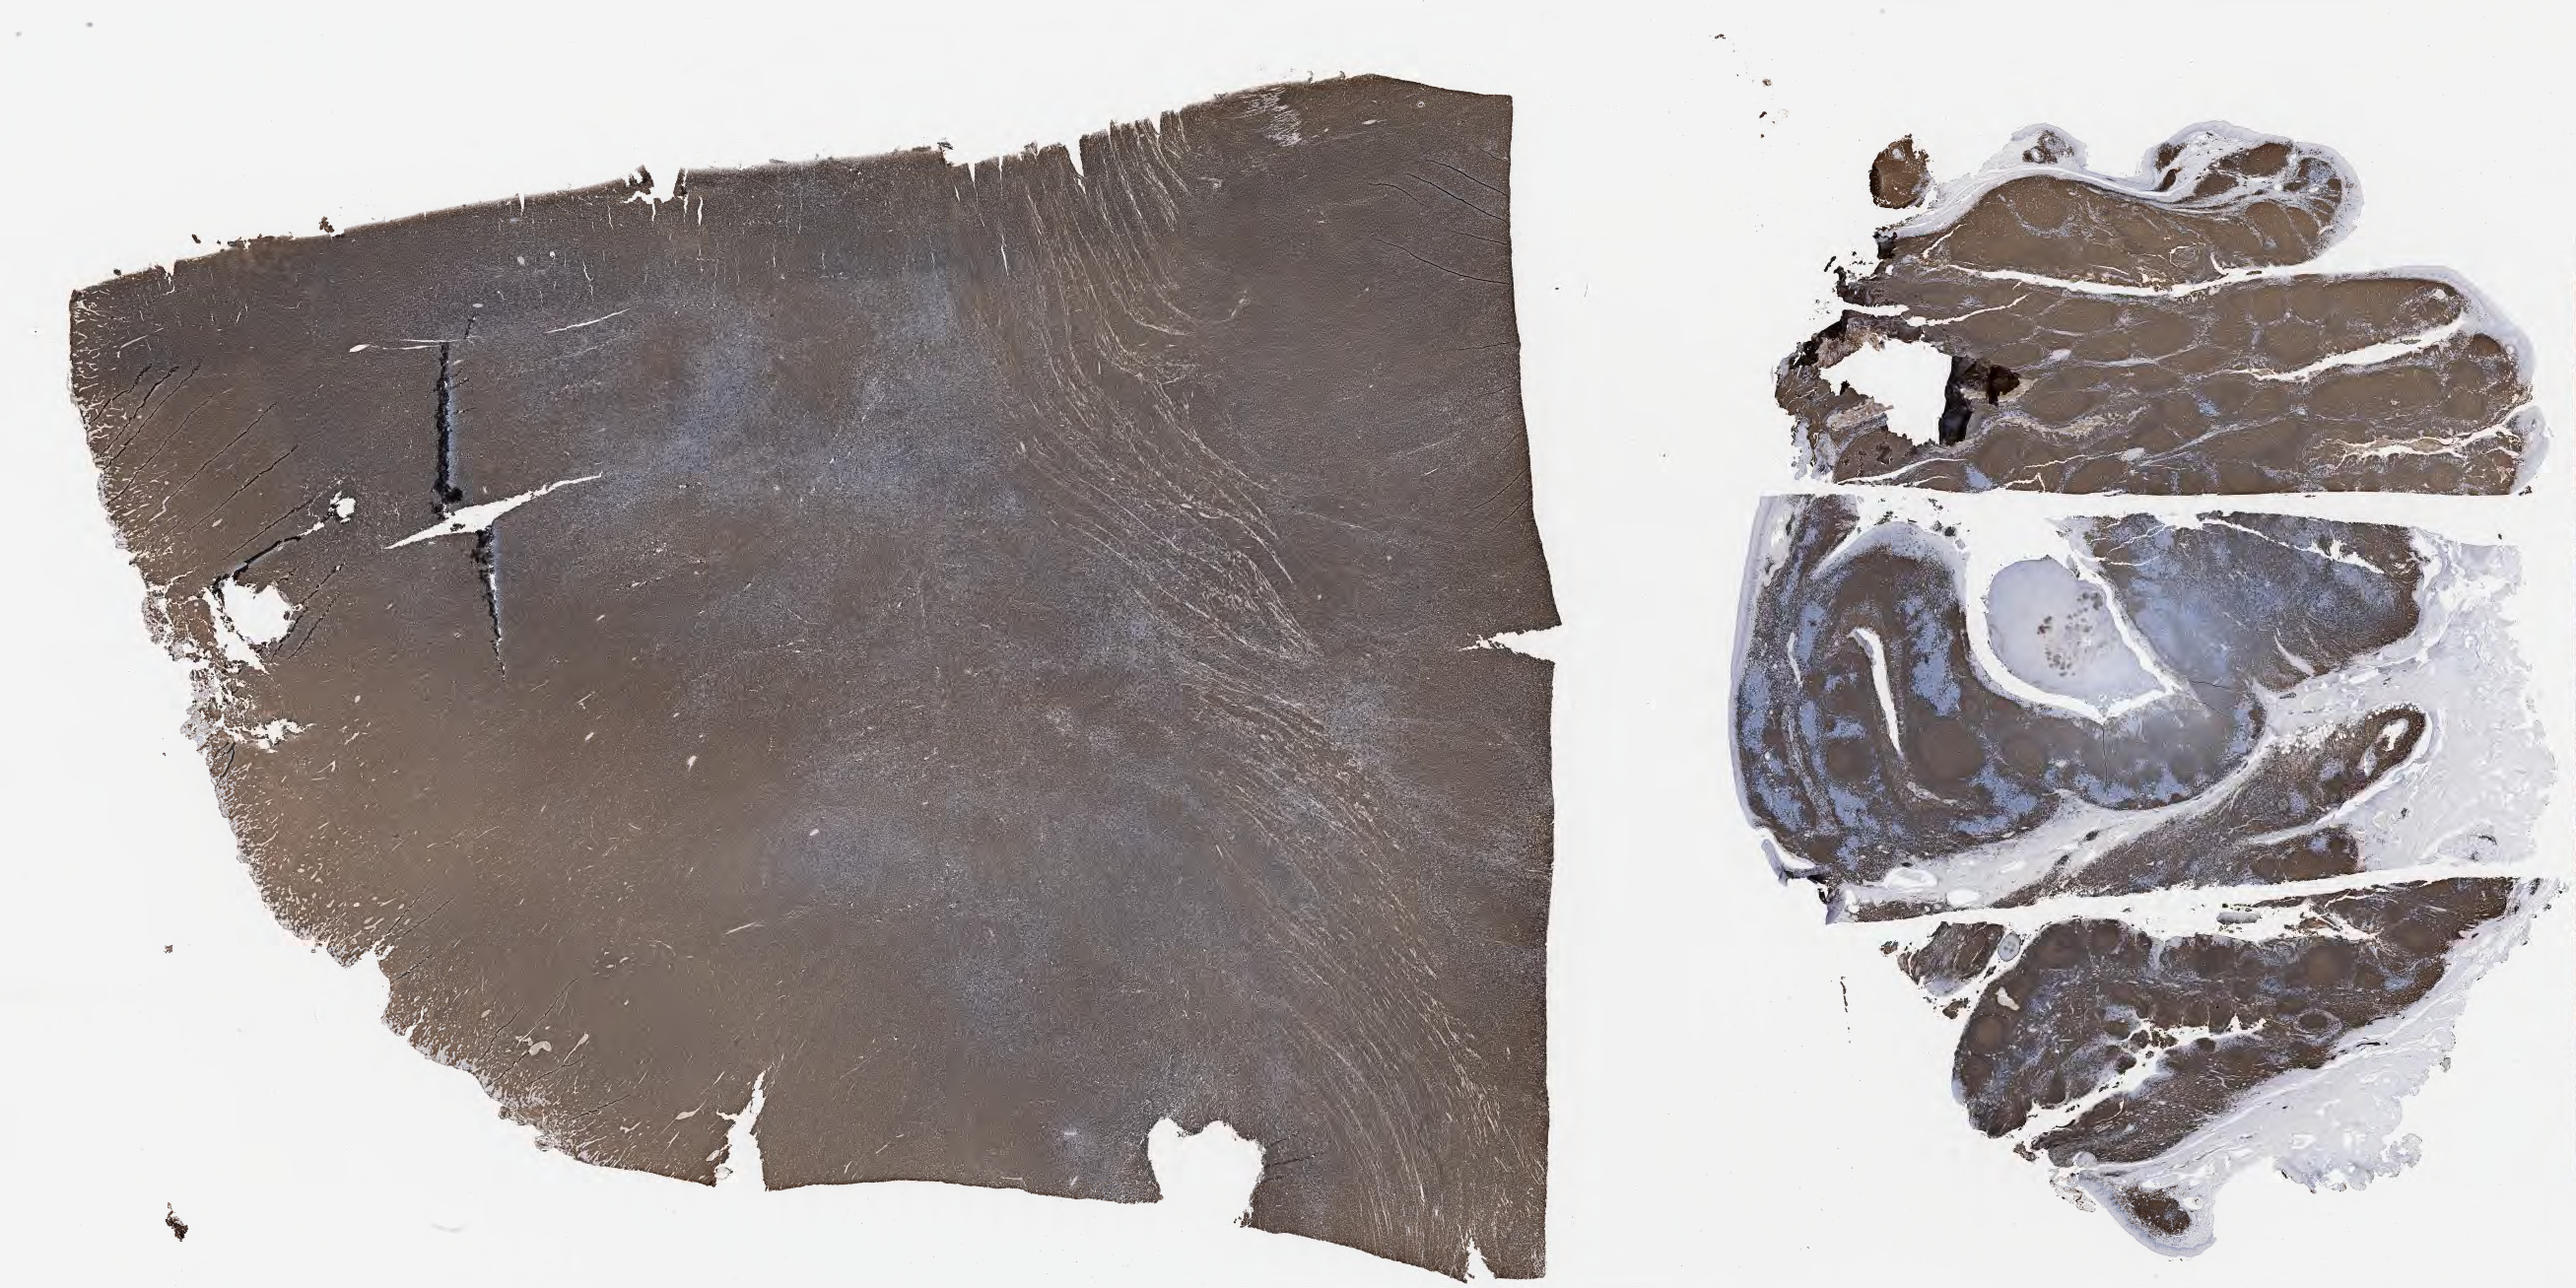
Immunohistochemistry (IHC) whole-slide image stained for CD20, whole scanned area (about 42.3 x 21.1 mm) shown as a low-resolution overview, specimen: tumor tissue. Male patient, age 17 years.
Histologic diagnosis: Burkitt lymphoma, NOS.